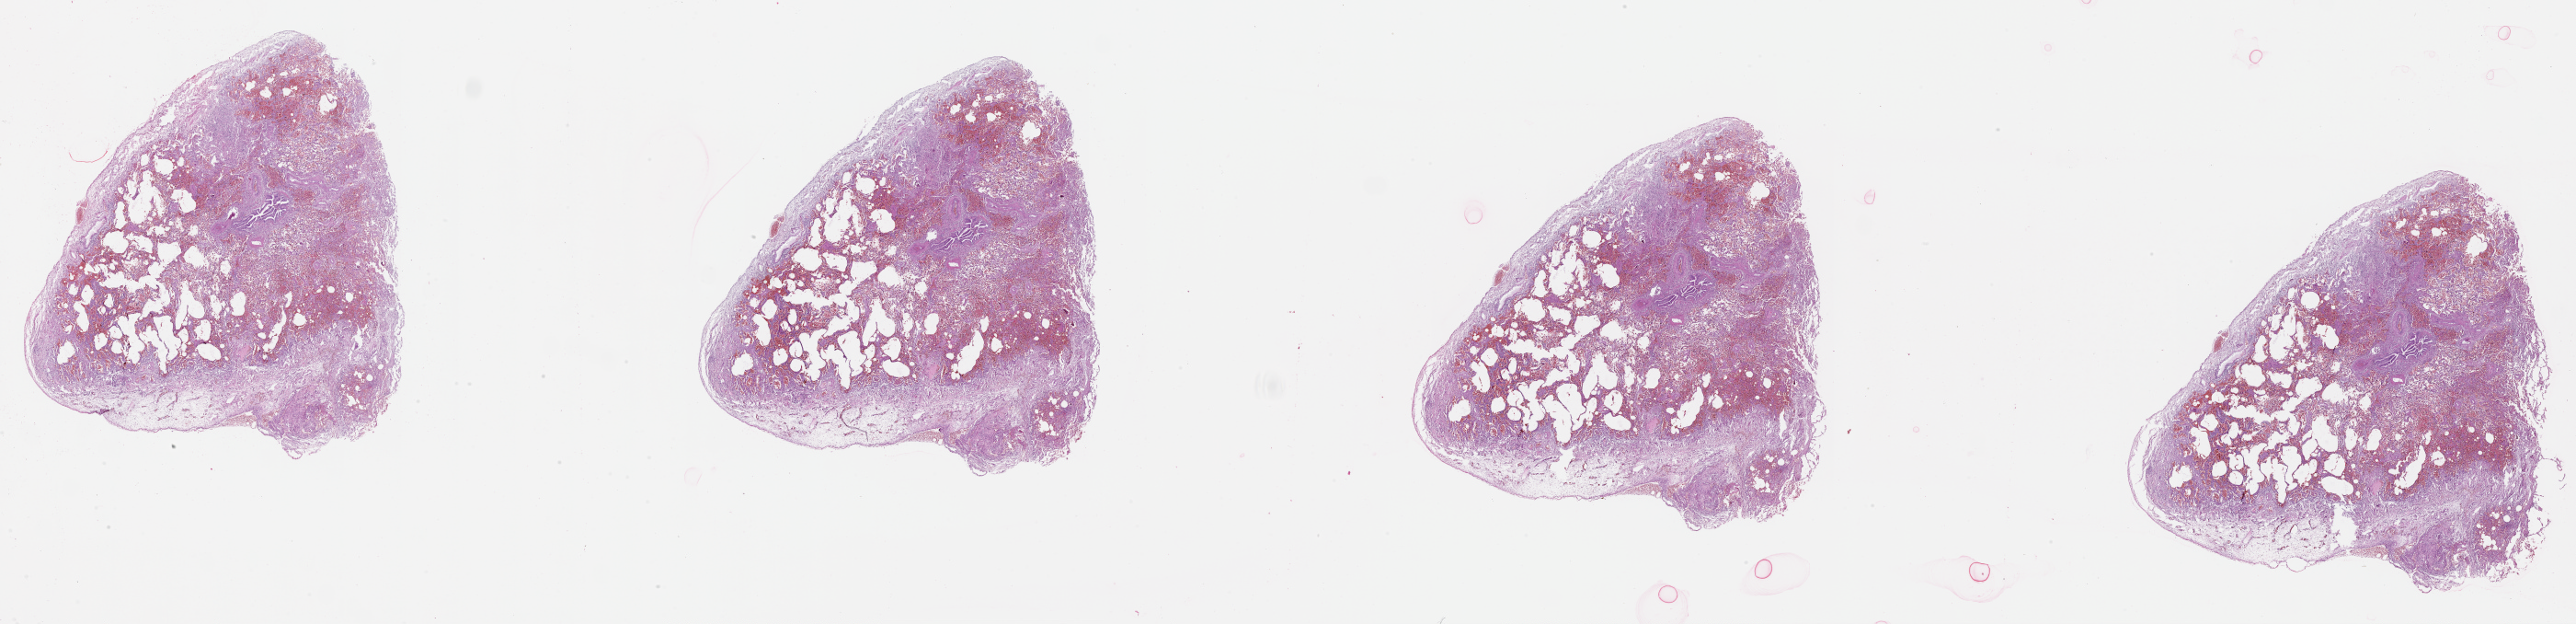
Whole-slide histology image, H&E, low-resolution overview of the scanned area, about 45.1 x 10.9 mm (slide scanned at 20x). Lung, normal (non-tumour) tissue. Male, 74 y/o.
This section: normal (non-tumour) tissue from the same patient. Patient diagnosis (cohort enrolment): squamous cell carcinoma (lung).